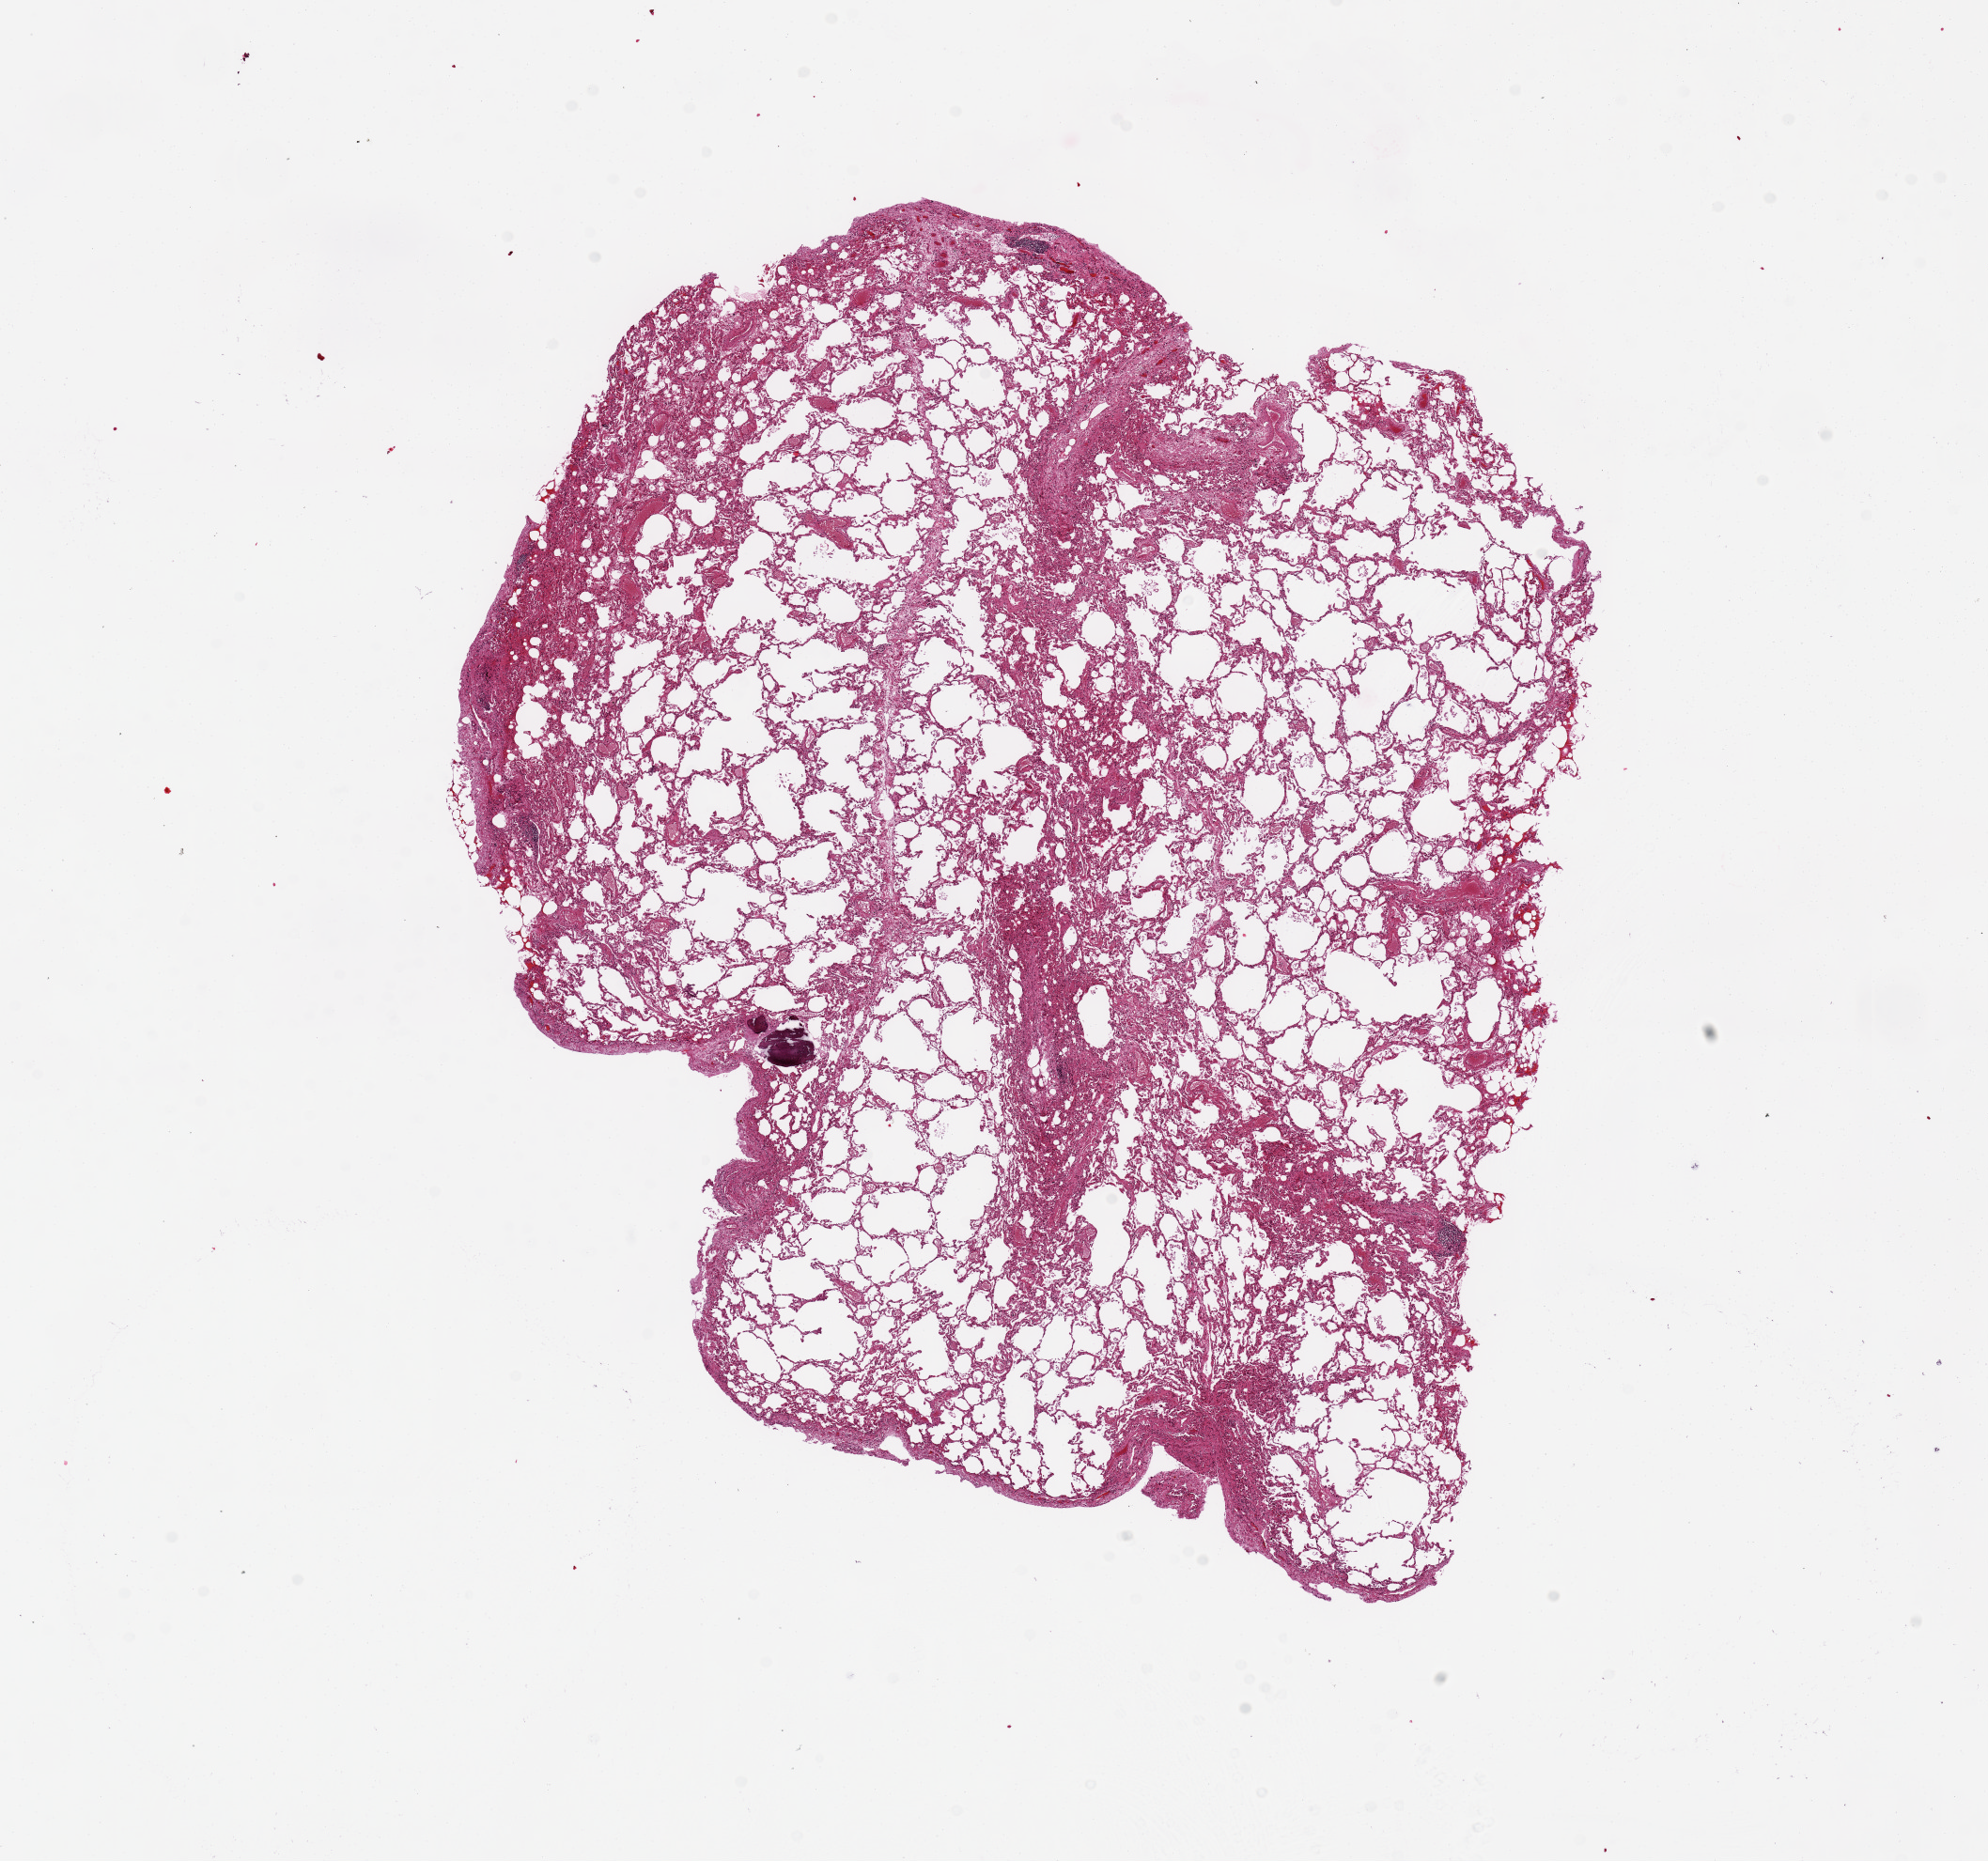
Digitized haematoxylin and eosin-stained section, a low-resolution overview of the entire scanned area, about 16.7 x 15.7 mm (acquisition: 20x scan); PAXgene-fixed, paraffin-embedded tissue; sampled site (target tissue): lung; tissue donor sample. Female donor.
• pathologist's review note for this sample: 10x9 mm